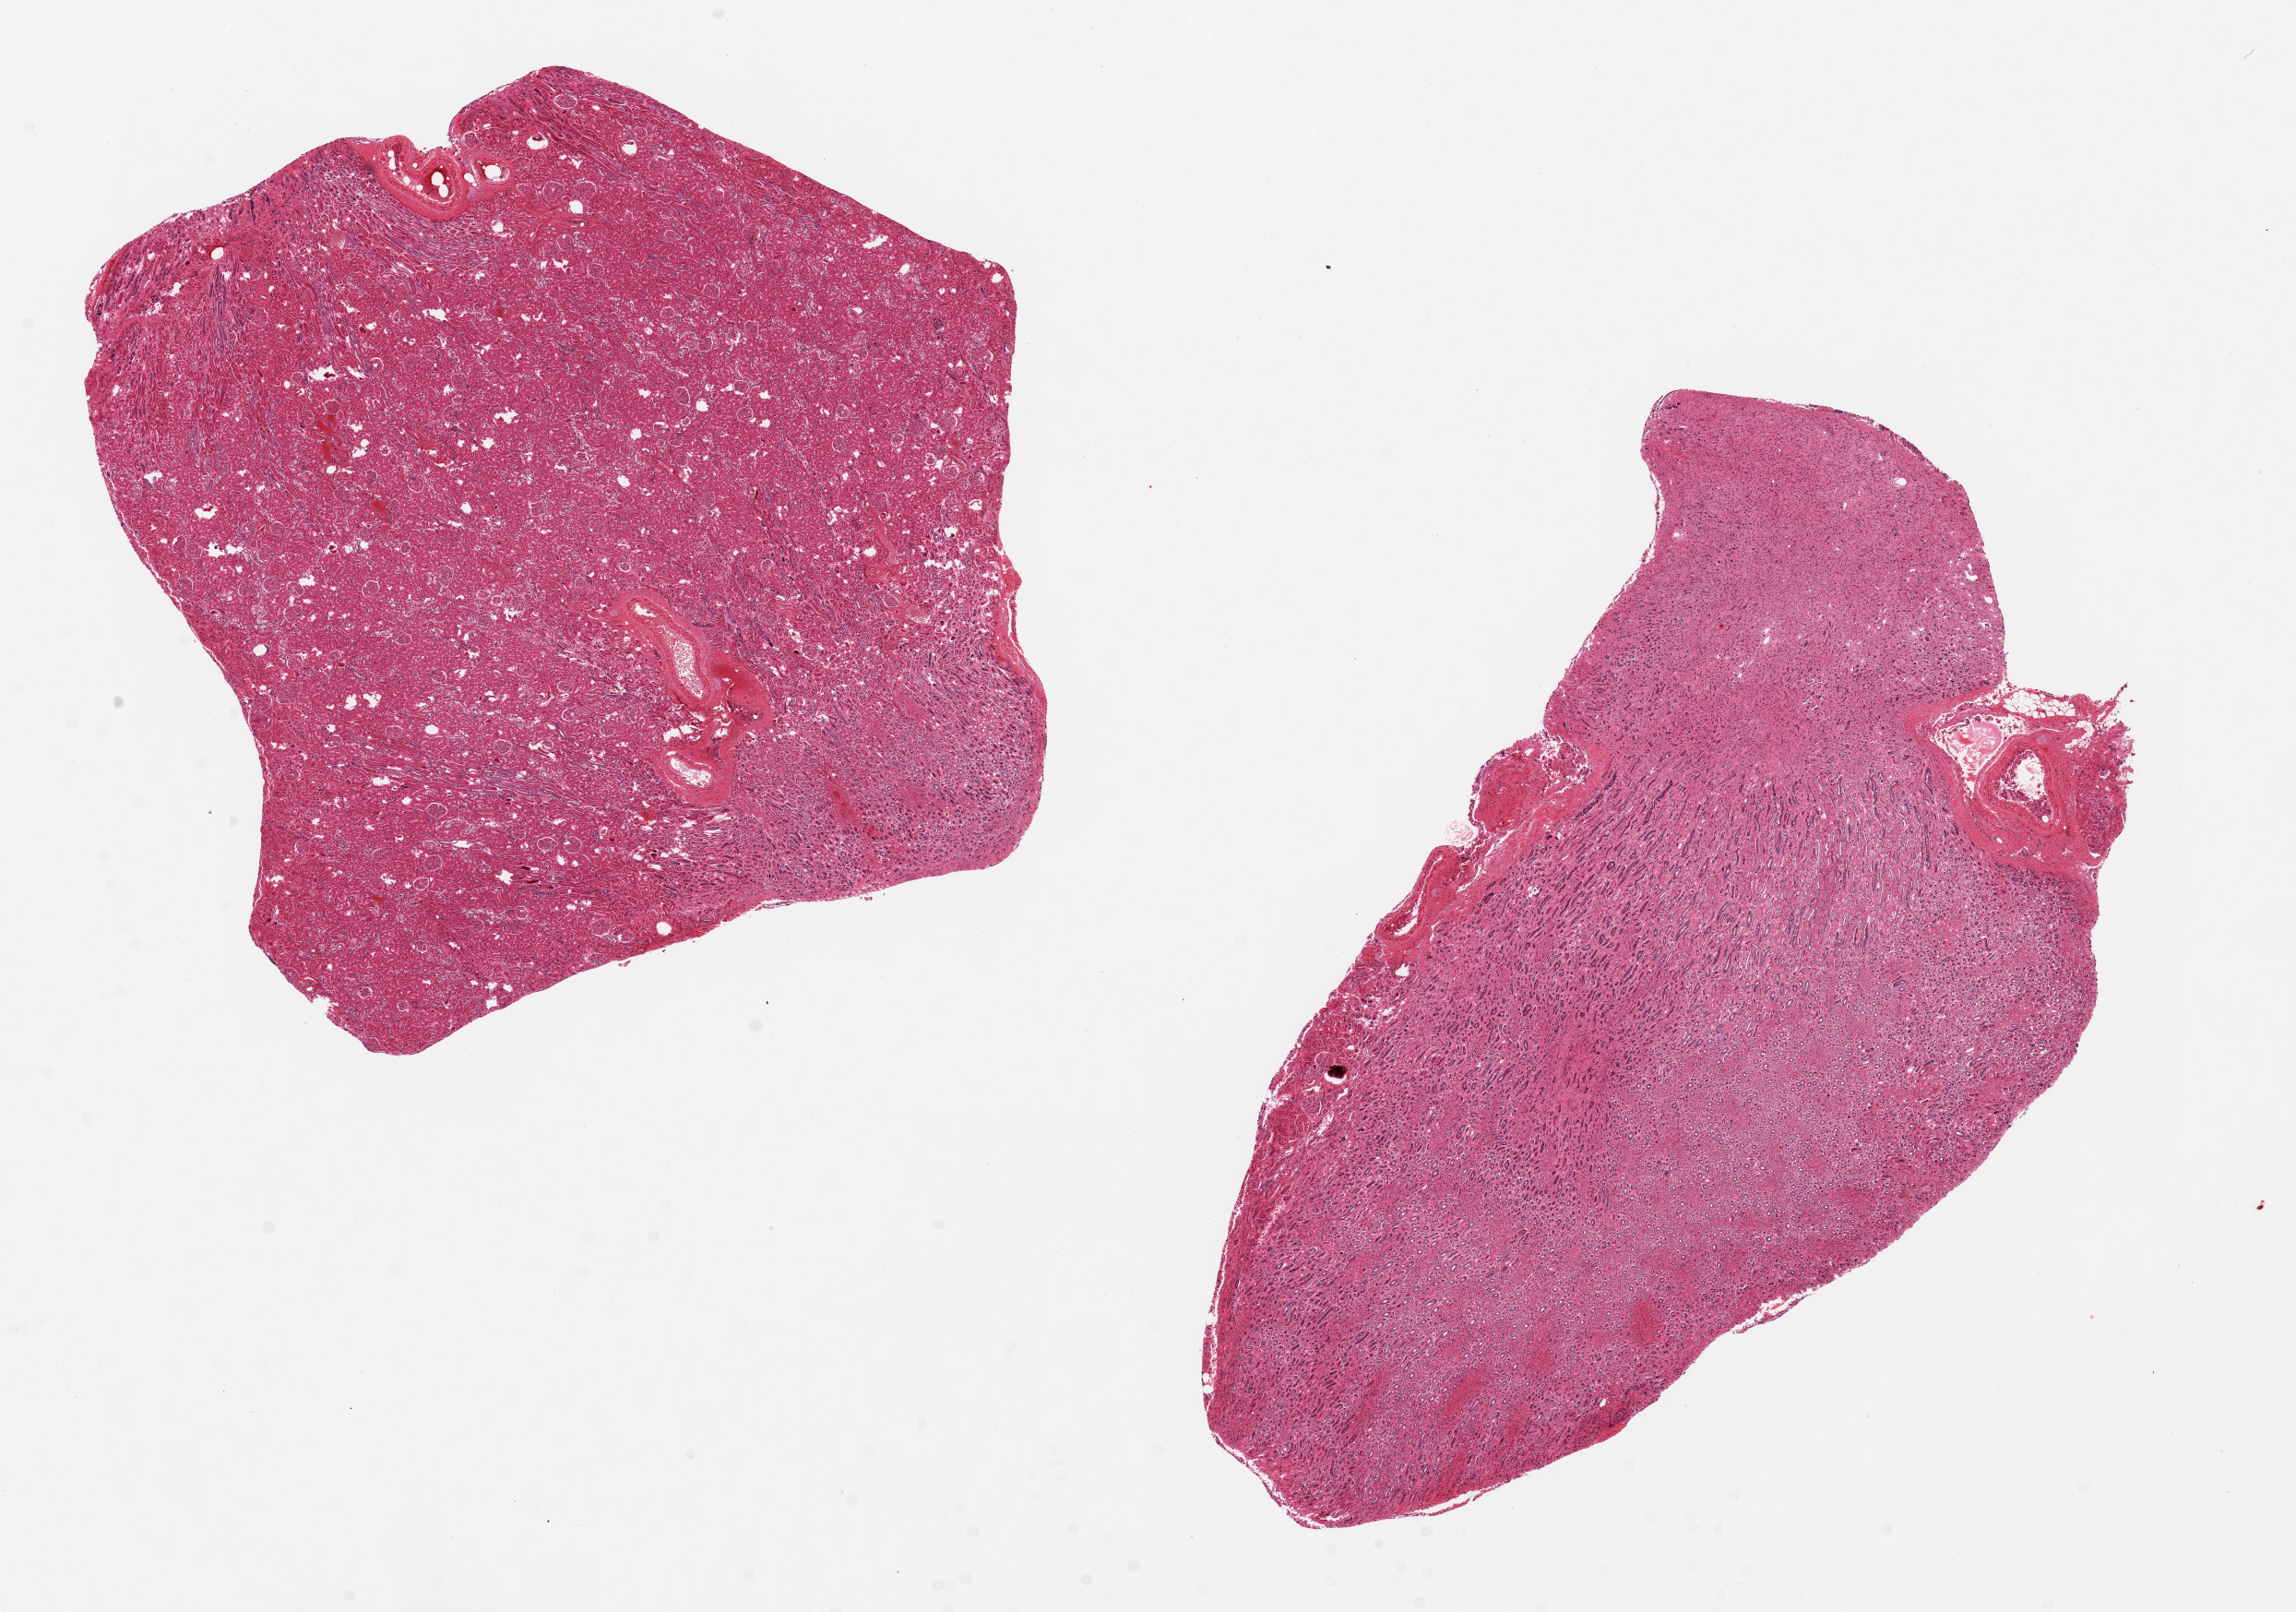
Haematoxylin and eosin whole-slide image — low-resolution overview of the scanned area, about 19.7 x 13.8 mm; PAXgene-fixed paraffin-embedded (PFPE) section; target tissue: renal medulla; donor tissue sample. Donor: male.
- reviewer comment on this tissue sample: 2 pieces, 7.5x7.5 mm & 10x5 mm; 10x5mm is all medulla; 7.5 square piece is 25% medulla, 75% cortex